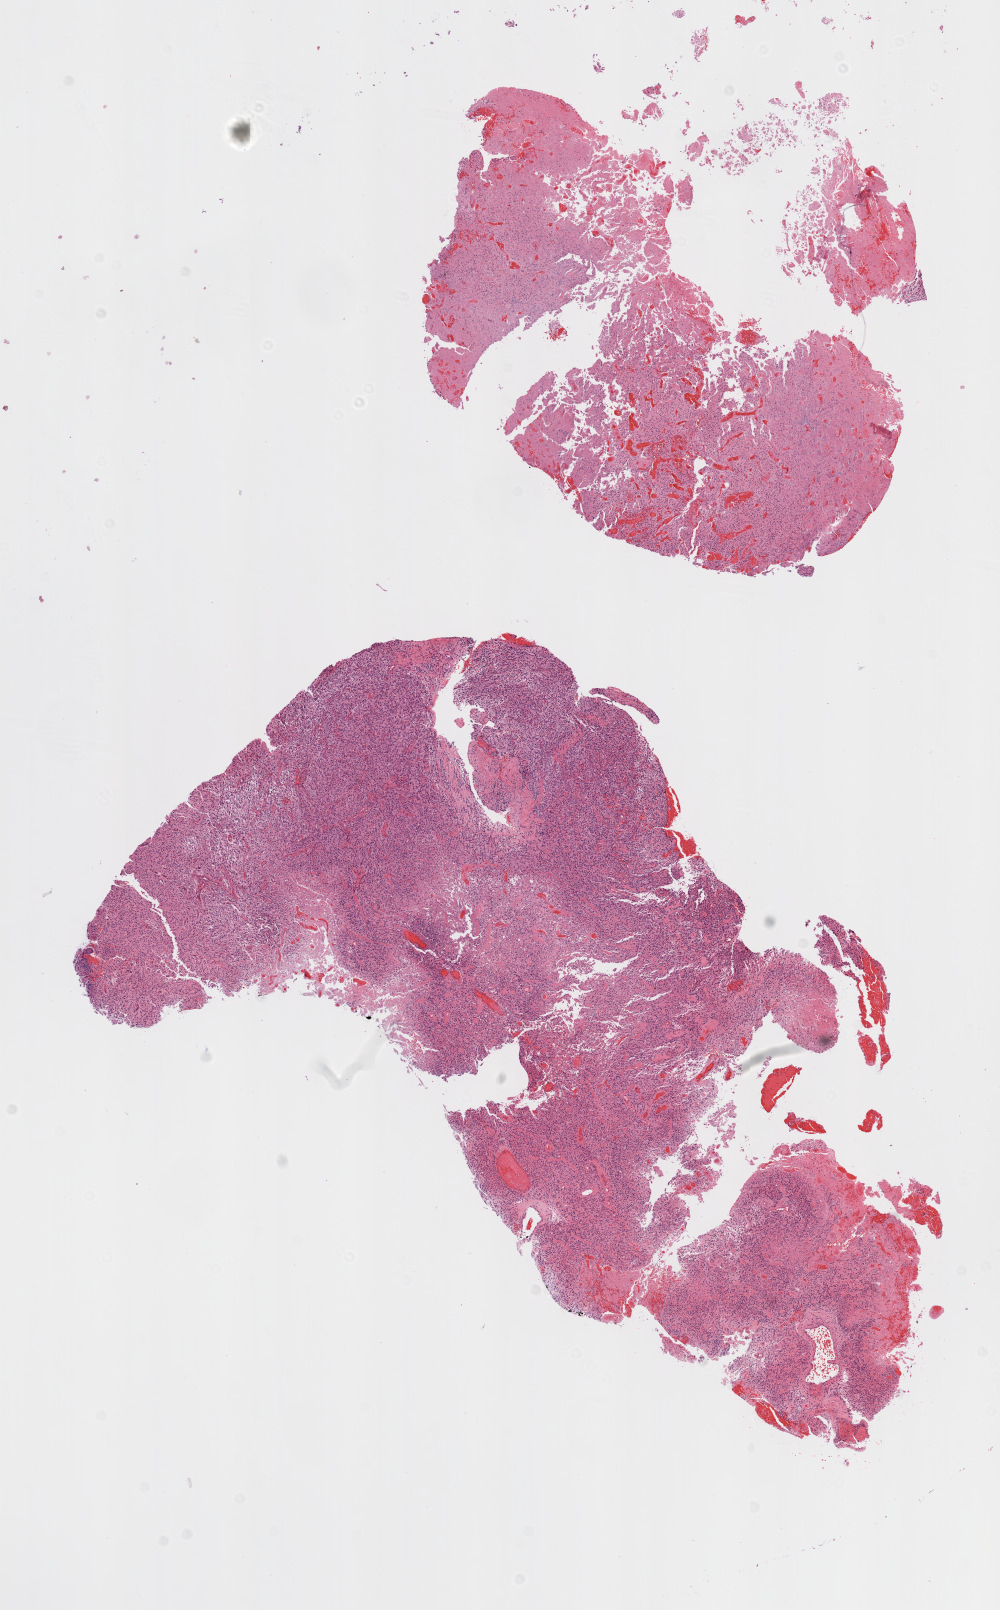
Digitized Hematoxylin and eosin (H&E) stained tissue section (whole slide) — a low-resolution overview of the entire scanned area, about 8.0 x 12.9 mm (slide scanned at 20x), formalin-fixed paraffin-embedded (FFPE) diagnostic section, sample: primary tumour, brain. Patient: female, age at initial diagnosis 63 years.
Diagnosis: Glioblastoma.